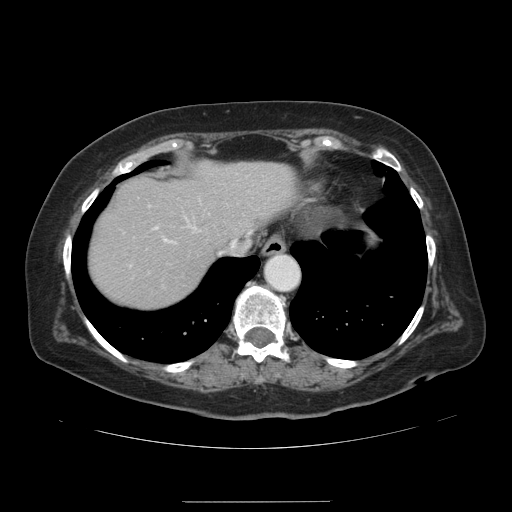
Contrast-enhanced abdominal CT, one axial slice. 120 kVp. Intravenous contrast given. Soft-tissue window (W 400 / L 40 HU). 512 × 512 image matrix, field of view 393 × 393 mm. Female patient, age 74 years. Case-level facts recorded for this patient, not image findings: diagnosis: colorectal cancer liver metastases, imaged before liver resection; multiple liver metastases: yes; largest metastasis: 7 cm; disease in both lobes: yes.
Outlined on this slice (outlined manually by an expert reader):
- hepatic veins: box from (x=219, y=239) to (x=250, y=254) px
- liver: (x=90, y=161)–(x=295, y=309)
- planned liver remnant (the part of the liver to remain after resection): (x=90, y=161)–(x=295, y=309)
- portal vein (with intrahepatic branches): (x=155, y=226)–(x=250, y=242)